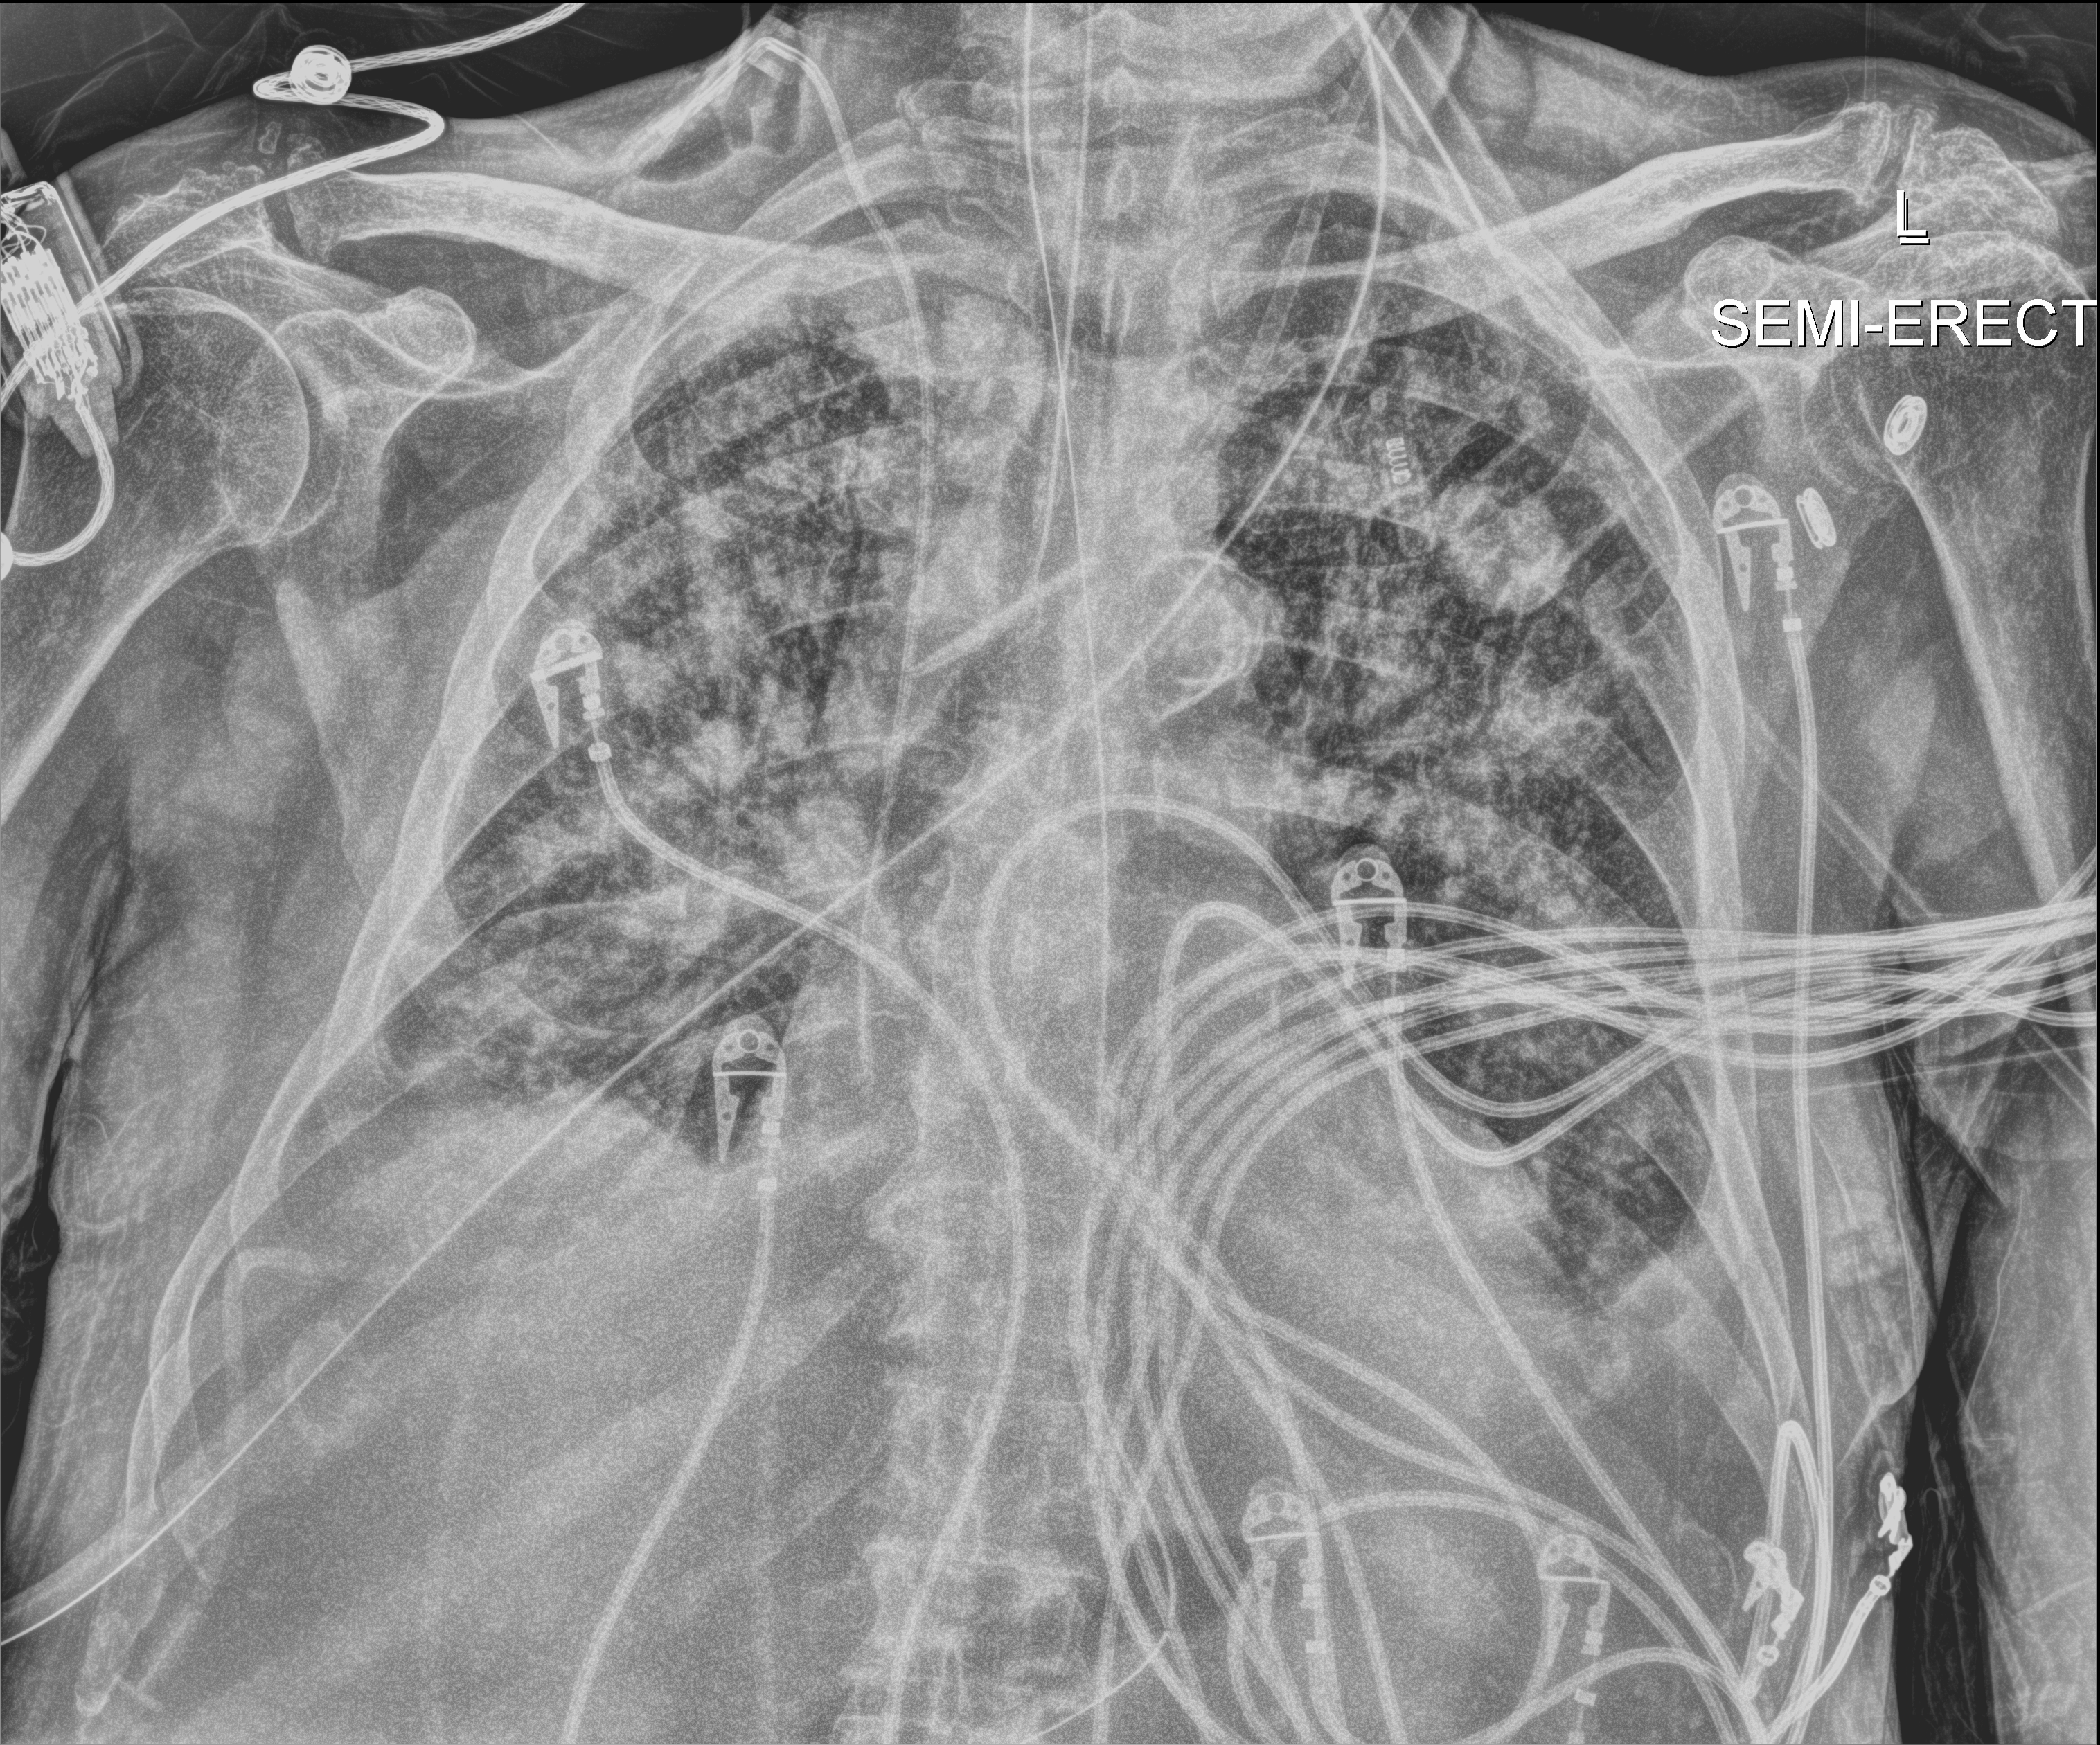
Bedside chest radiograph (digital radiography). Male patient hospitalised with COVID-19, age 75–90 years.
From the hospital-stay record, not from the radiograph (when in the stay this image was taken is not recorded): other chronic lung disease (admission record): no; length of hospital stay: 28 days.